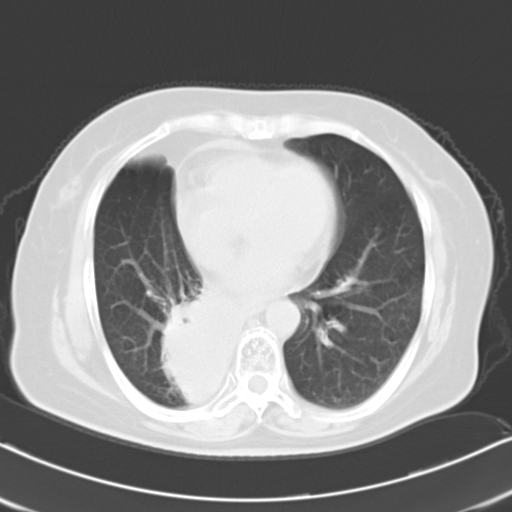
Chest CT, one axial slice. Position 8 of 21 along the scan axis. Reconstruction kernel B40f. 120 kVp. Lung window (W 1500 / L -600 HU). 512 × 512 image matrix, field of view 326 × 326 mm. Patient: female, 61 years. Case-level facts recorded for this patient, not image findings: clinical TNM (as recorded): T1b N0 M1b.
Annotated regions visible in this slice (bounding box drawn by a radiologist):
- lung tumour (recorded histology: squamous cell carcinoma): bounding box [x1, y1, x2, y2] px = [138, 262, 245, 425]